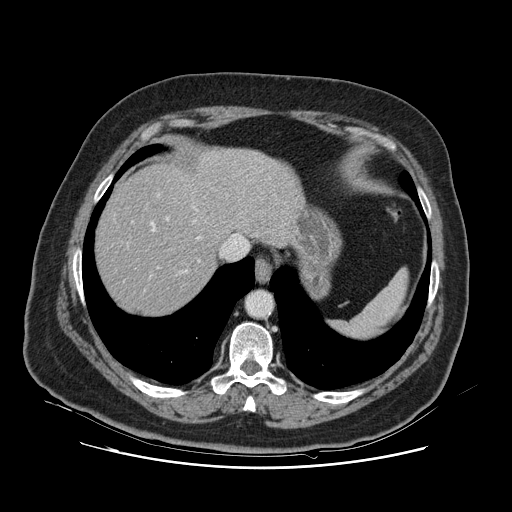
Contrast-enhanced abdominal CT, one axial slice. Position 102 of 132 along the scan axis. 120 kVp. Intravenous contrast given. Soft-tissue window (W 400 / L 40 HU). 2.5 mm slice thickness. 512 × 512 image matrix, field of view 391 × 391 mm. Female patient, age 73 years. Case-level facts recorded for this patient, not image findings: diagnosis: colorectal cancer liver metastases, imaged before liver resection; multiple liver metastases: no.
Annotated regions visible in this slice (manually delineated by an expert):
- hepatic veins: bounding box (x1, y1, x2, y2) in pixels: (131, 206, 200, 278)
- liver: (96, 149, 297, 315)
- planned liver remnant (the part of the liver to remain after resection): (96, 166, 229, 315)
- portal vein (with intrahepatic branches): (158, 194, 169, 268)